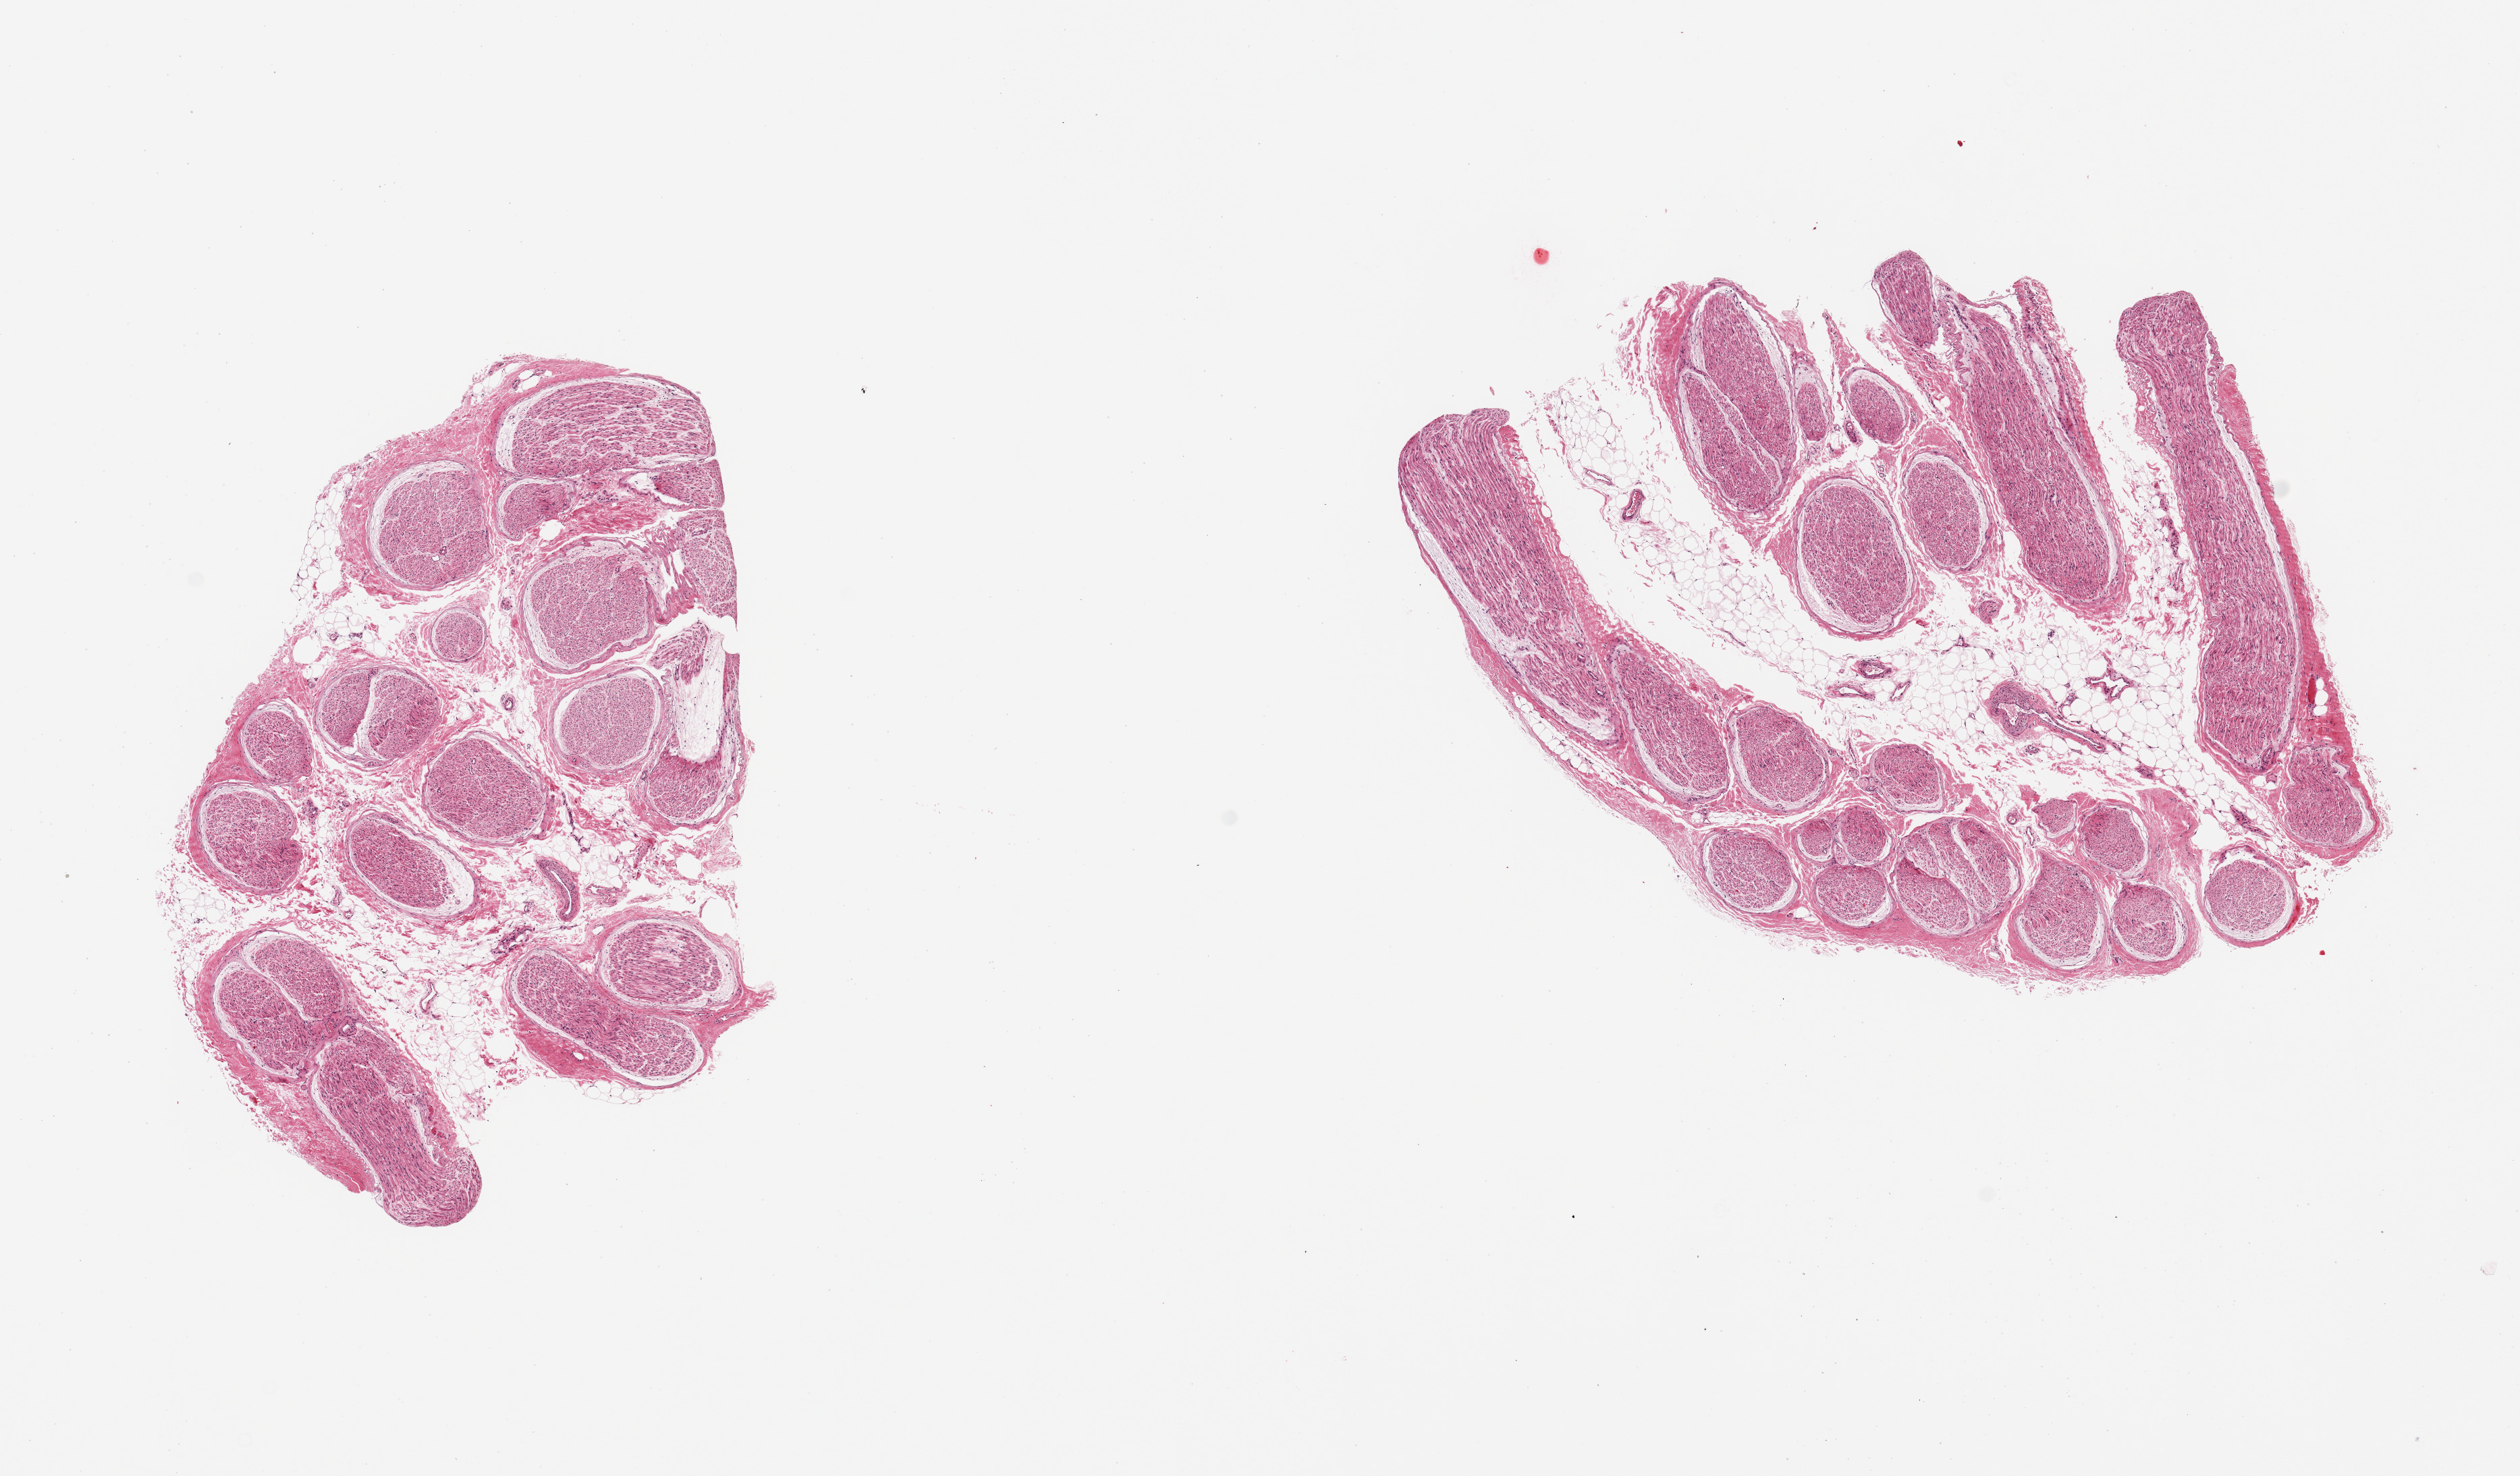
Hematoxylin and eosin (H&E) whole-slide image, brightfield, whole scanned area (about 14.8 x 8.6 mm, from a 20x scan) shown as a low-resolution overview, PAXgene-fixed, paraffin-embedded tissue, sampled site (target tissue): tibial nerve, tissue donor sample. Female donor.
Pathologist's review note for this sample: 2 pieces; well trimmed externally, but with internal fat content of 25%.